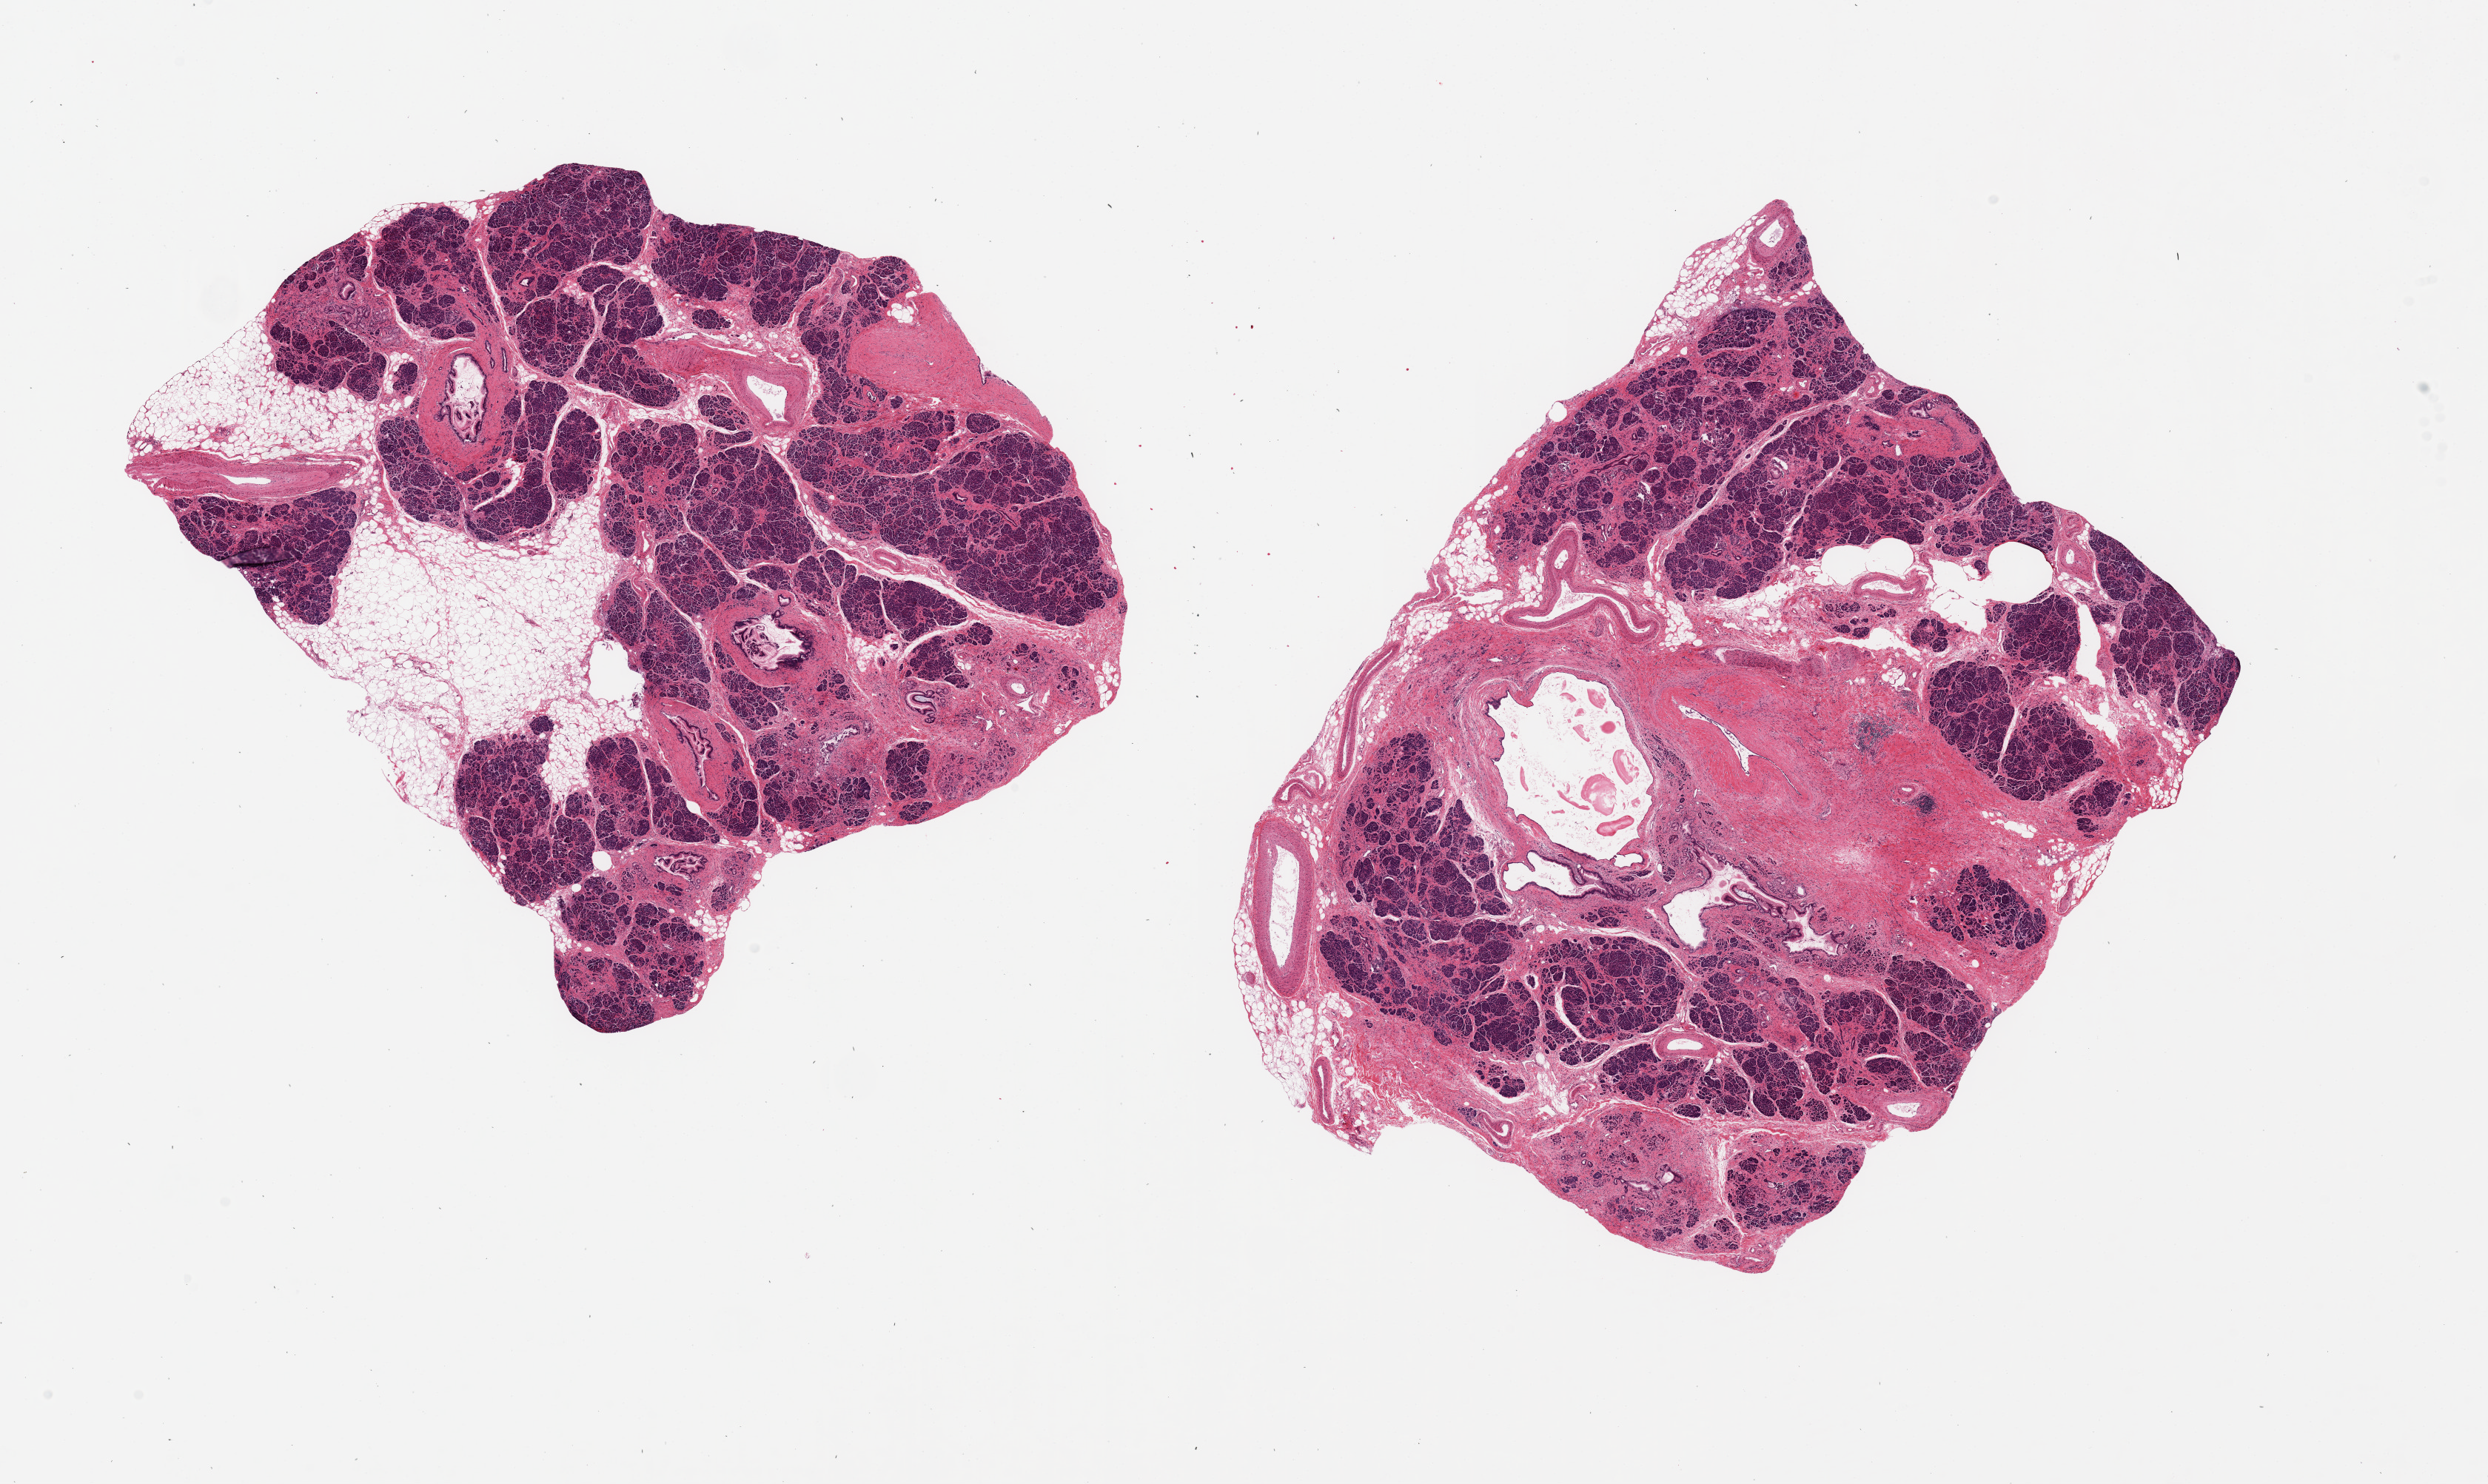
Digitized haematoxylin and eosin-stained section, a low-resolution overview of the entire scanned area, about 26.6 x 15.9 mm; PAXgene-fixed paraffin-embedded (PFPE) section; target tissue: pancreas; tissue donor sample. Donor sex: male.
* reviewer comment on this tissue sample: 2 pieces, ~8x8mm, ~50% fibrosis/fat, evidence of old pancreatitis